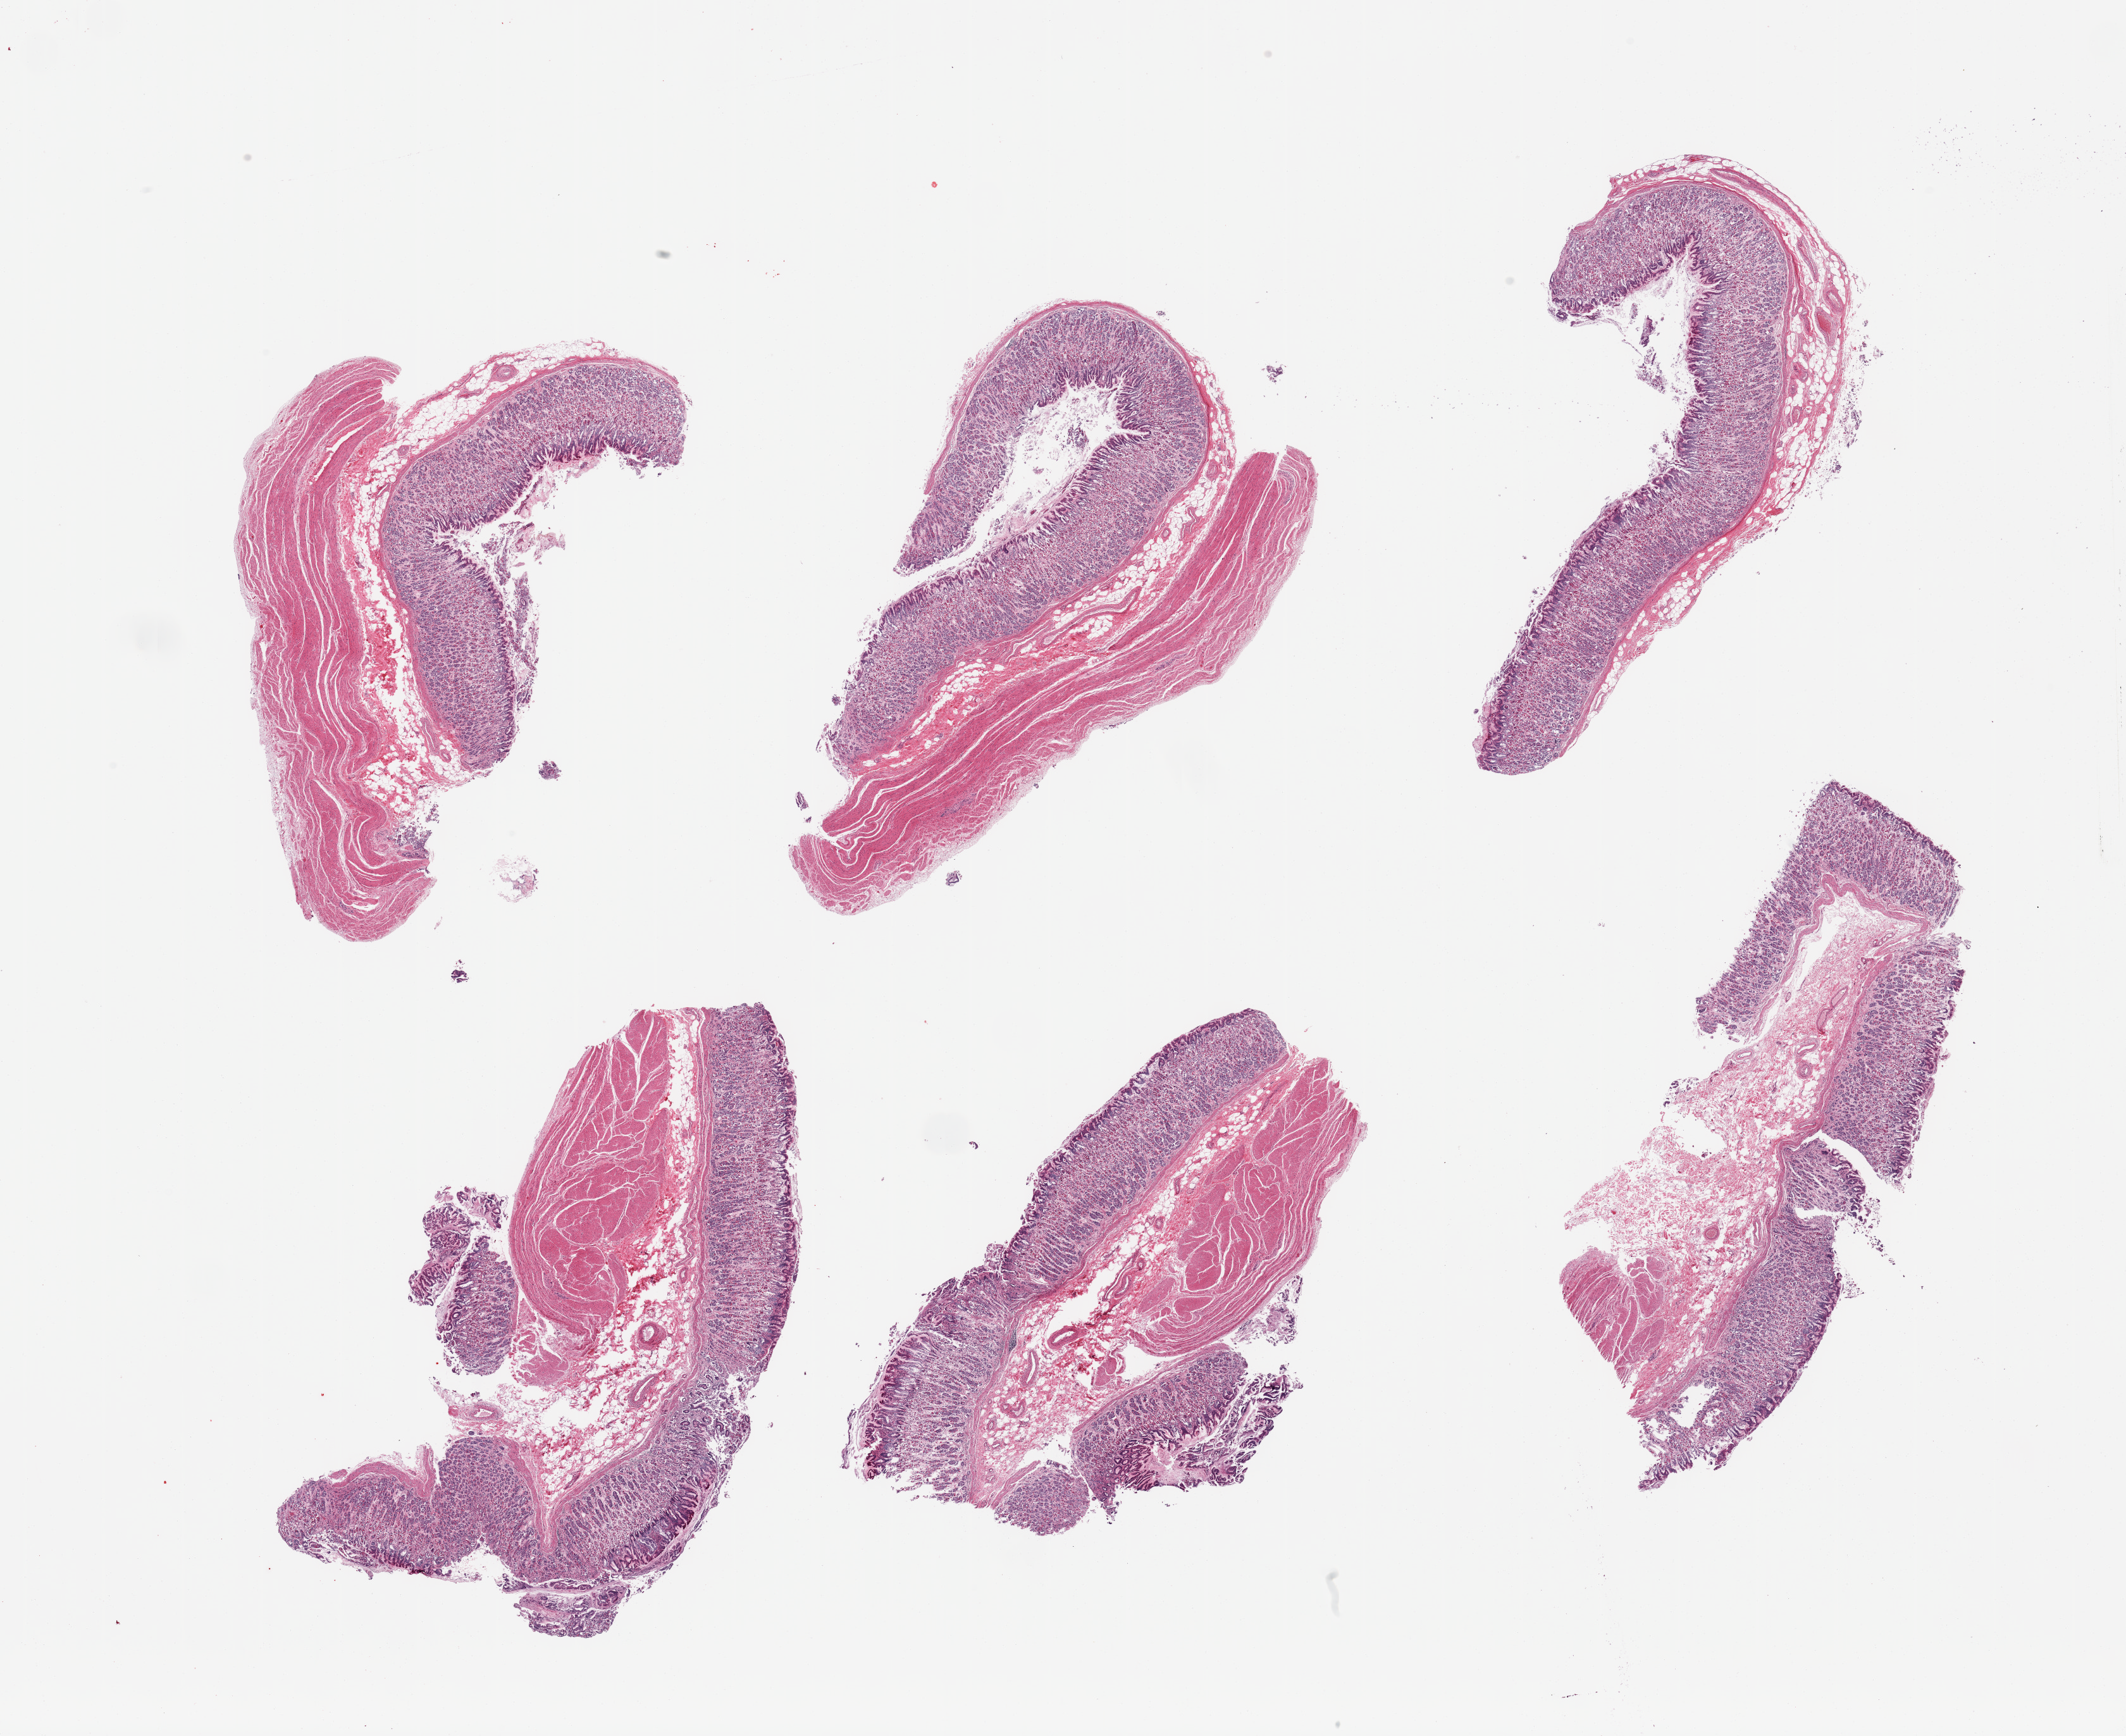
Whole-slide image, H&E stain — whole scanned area (about 26.6 x 21.7 mm) shown as a low-resolution overview, PAXgene-fixed, paraffin-embedded tissue, section of stomach (target tissue), tissue donor sample.
Review note (as recorded): 6 pieces; variable representation of mucosa and muscularis.